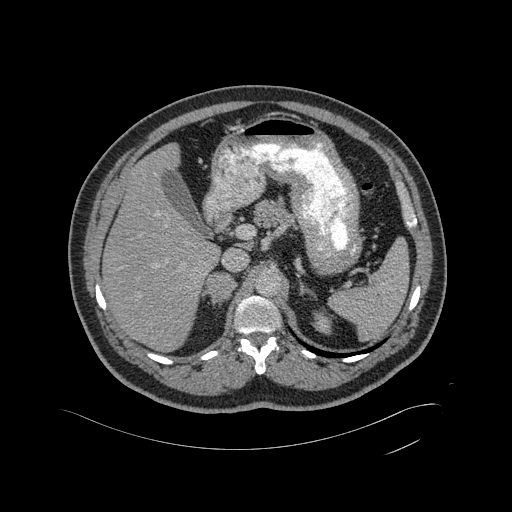
Contrast-enhanced abdominal CT, one axial slice. Position 319 of 433 along the scan axis. 120 kVp. Soft-tissue window (W 400 / L 40 HU). 512 × 512 image matrix, field of view 500 × 500 mm. Patient: male, 56 years. From the clinical record (not read from this slice): diagnosis: adrenocortical carcinoma; tumour side: right adrenal; tumour size at pathology: 11.6 cm; Ki-67 index: 50 %; stage (as recorded): 3.
Annotated regions visible in this slice (semi-automatically segmented with operator editing):
- mass: bounding box (x1, y1, x2, y2) in pixels: (207, 274, 235, 299)